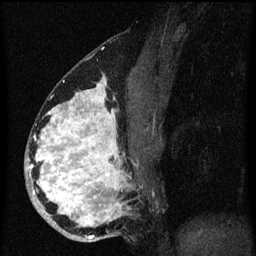
Breast MRI (dynamic contrast-enhanced), one sagittal slice; slice 31 of 60 in the series (ordered by position); dynamic contrast-enhanced series, image 2 of 3 at this slice position (ordered by acquisition); 1.5 T; TE 4.2 ms, TR 8.4 ms; 2 mm slice thickness; 256 × 256 image matrix, field of view 180 × 180 mm. Female patient, age 34 years. Case-level facts recorded for this patient, not image findings: setting: breast cancer imaged before/during neoadjuvant chemotherapy; receptor status: HR-positive, HER2-negative.
Outlined on this slice (semi-automatic segmentation, software-assisted and operator-edited):
- analysis volume of interest (the breast-tissue region the enhancement analysis was run in; not a lesion): box from (x=26, y=58) to (x=151, y=243) px
- tumour enhancement mask (voxels above the 70 % enhancement threshold inside the analysis volume of interest): (x=26, y=80)–(x=131, y=239)